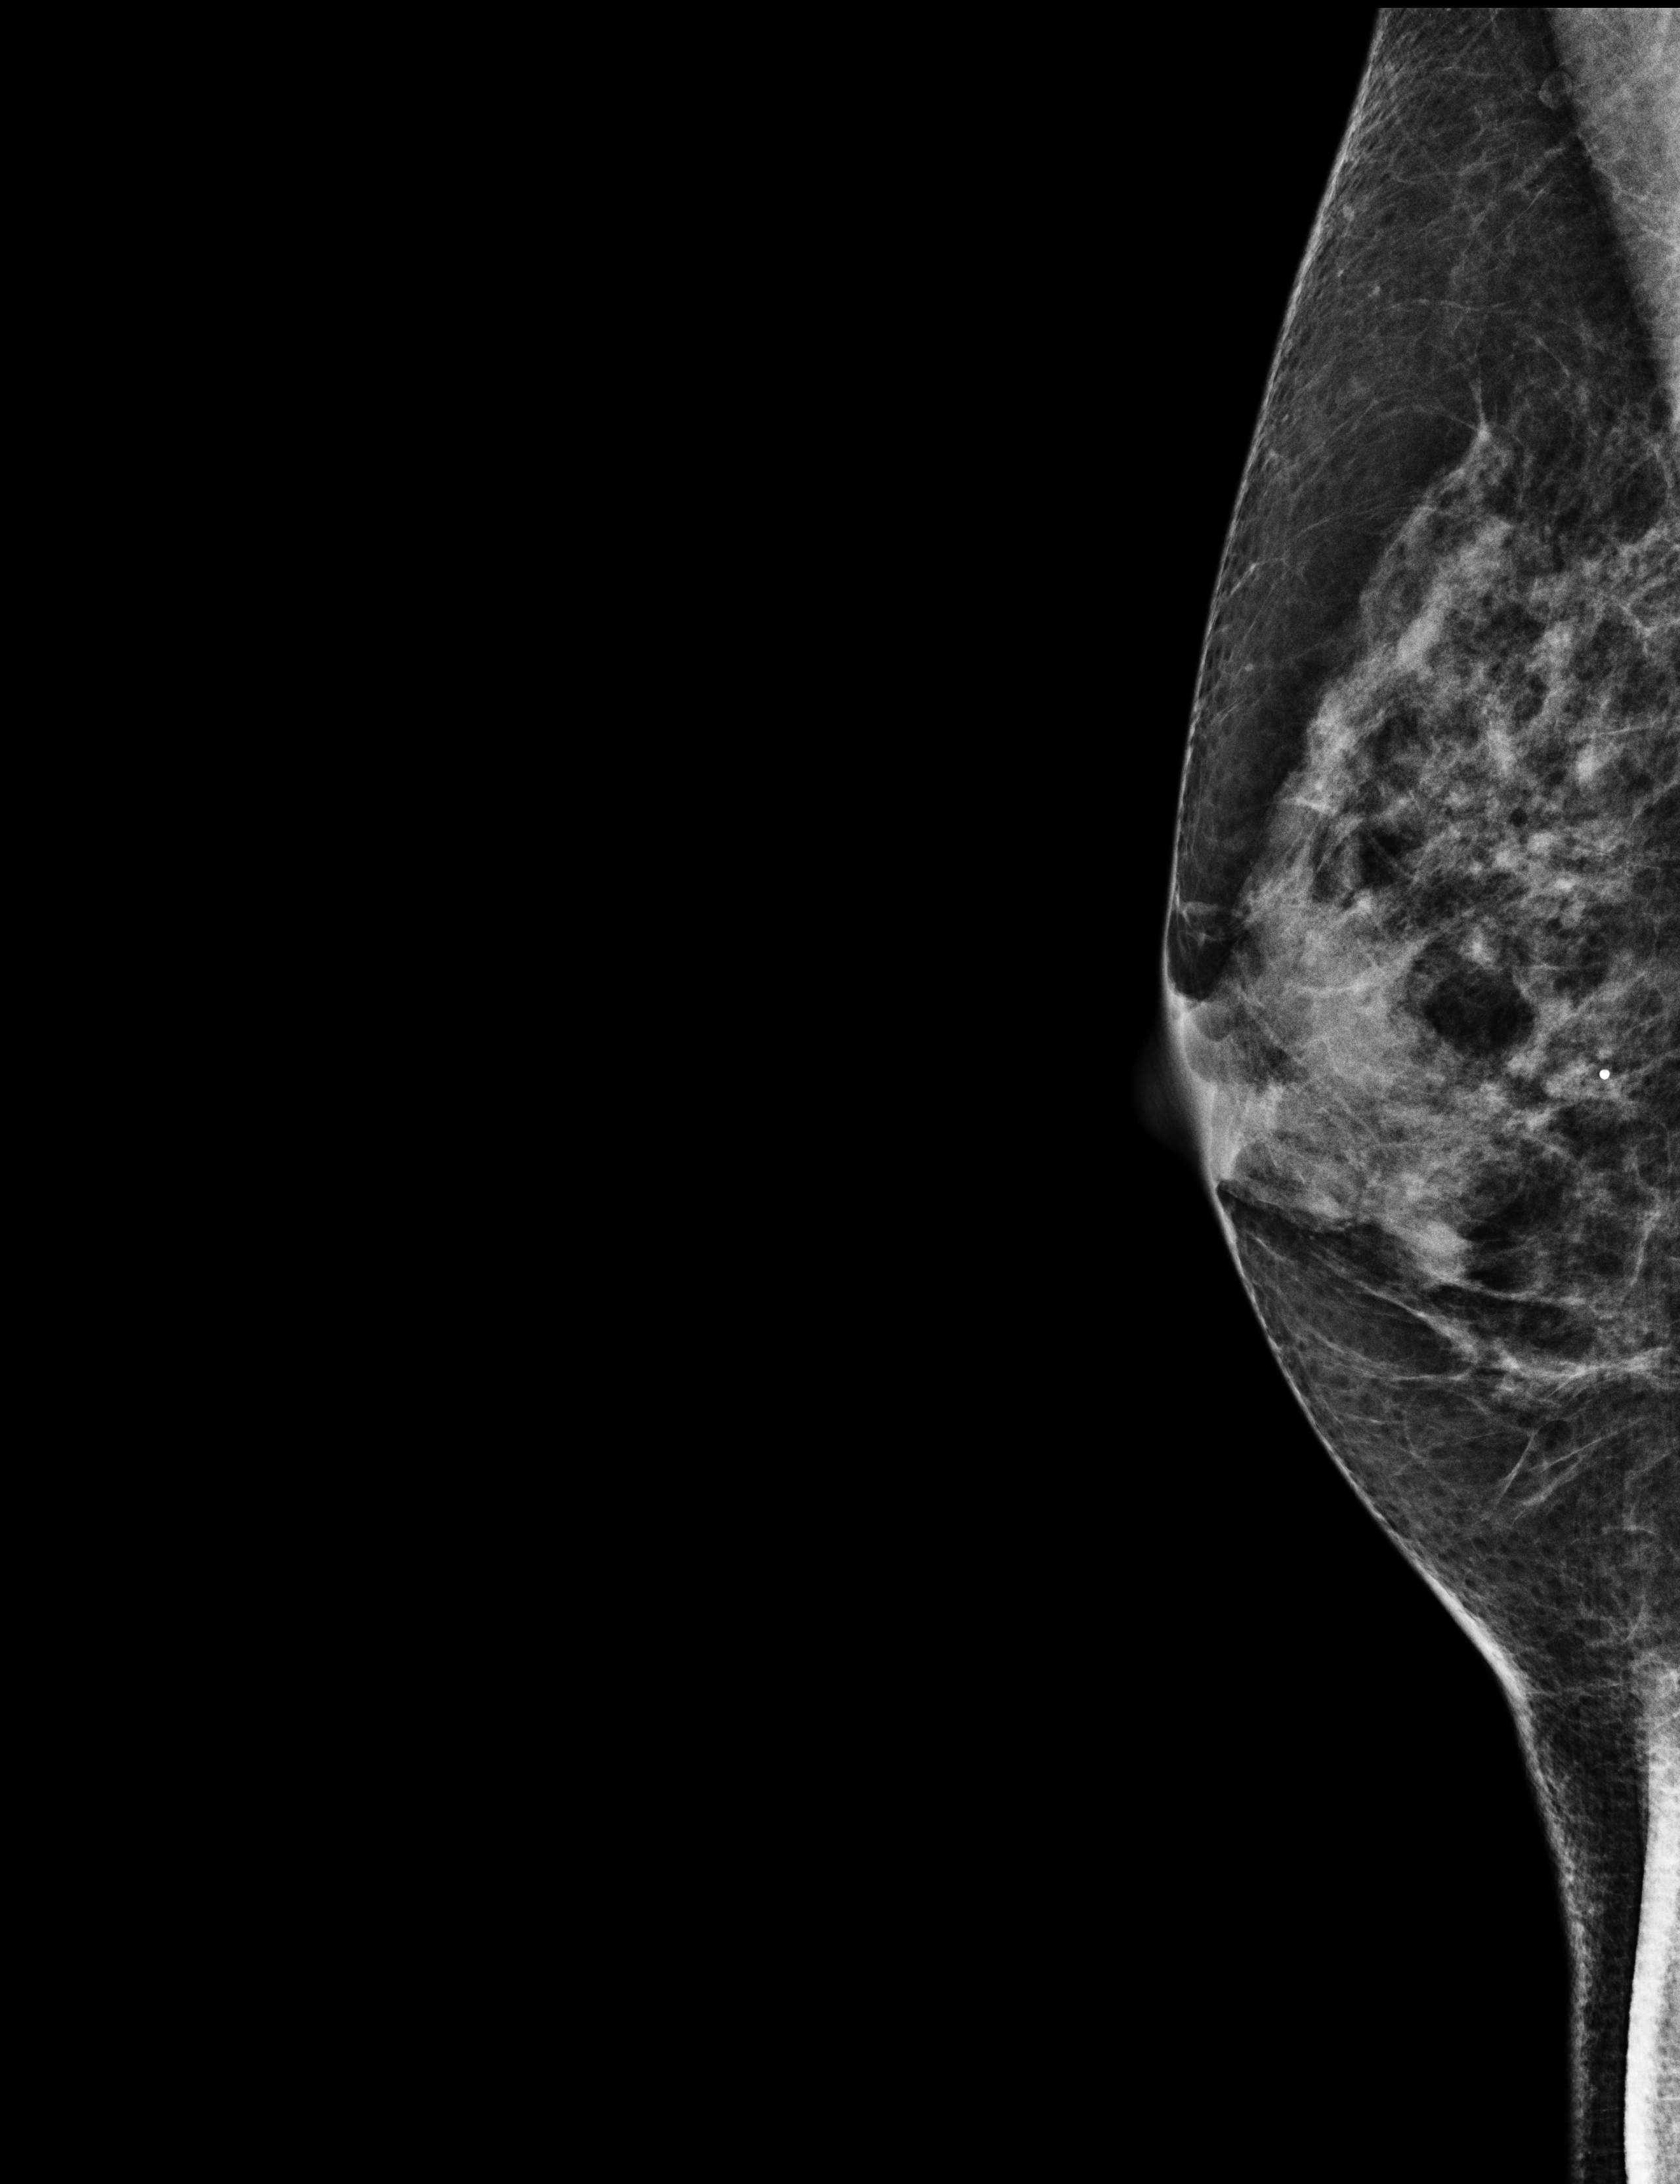
Digital mammogram (FFDM); right breast; mediolateral (ML) view; screening examination; system: Selenia Dimensions. Female patient, age 59 years.
BI-RADS breast density category at the screening exam (both breasts, scale 1–4): 3. Final BI-RADS assessment for this screening round (tomosynthesis exam, both breasts): category 1. Recall: no recall after this screen.